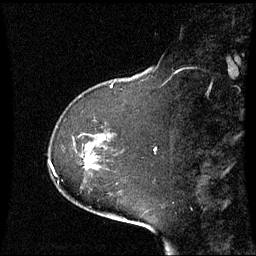
Breast MRI (dynamic contrast-enhanced), one sagittal slice. Dynamic contrast-enhanced series, image 2 of 3 at this slice position (ordered by acquisition). 1.5 T. TE 4.2 ms, TR 8.9 ms. 2.4 mm slice thickness. 256 × 256 image matrix, field of view 230 × 230 mm. Female patient, age 51 years. From the clinical record (not read from this slice): setting: breast cancer imaged before/during neoadjuvant chemotherapy; receptor status: HR-positive, HER2-negative.
Annotated regions visible in this slice (semi-automatically segmented with operator editing):
- analysis volume of interest (the breast-tissue region the enhancement analysis was run in; not a lesion): box from (x=73, y=134) to (x=111, y=169) px
- tumour enhancement mask (voxels above the 70 % enhancement threshold inside the analysis volume of interest): (x=86, y=157)–(x=88, y=160)